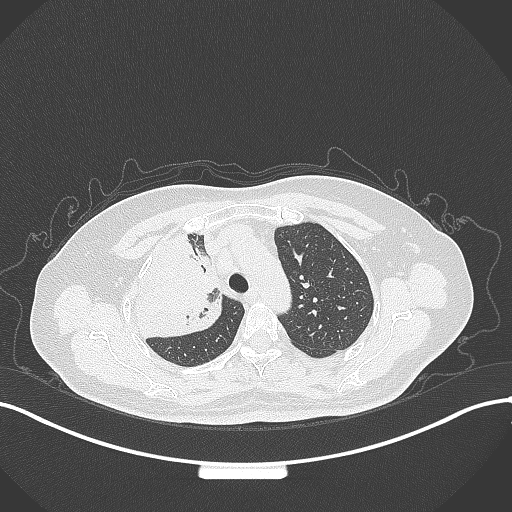
Chest CT, one axial slice; position 239 of 309 along the scan axis; reconstruction kernel B70f; lung window (W 1500 / L -600 HU); 1 mm slice thickness; 512 × 512 image matrix, field of view 400 × 400 mm. Female patient, age 60 years. From the clinical record (not read from this slice): clinical TNM (as recorded): T3 N1 M1.
Structures marked on this image (rectangle marked by the reading radiologist):
- lung tumour (recorded histology: adenocarcinoma): bounding box <123,234,228,343> (left, top, right, bottom; pixels)